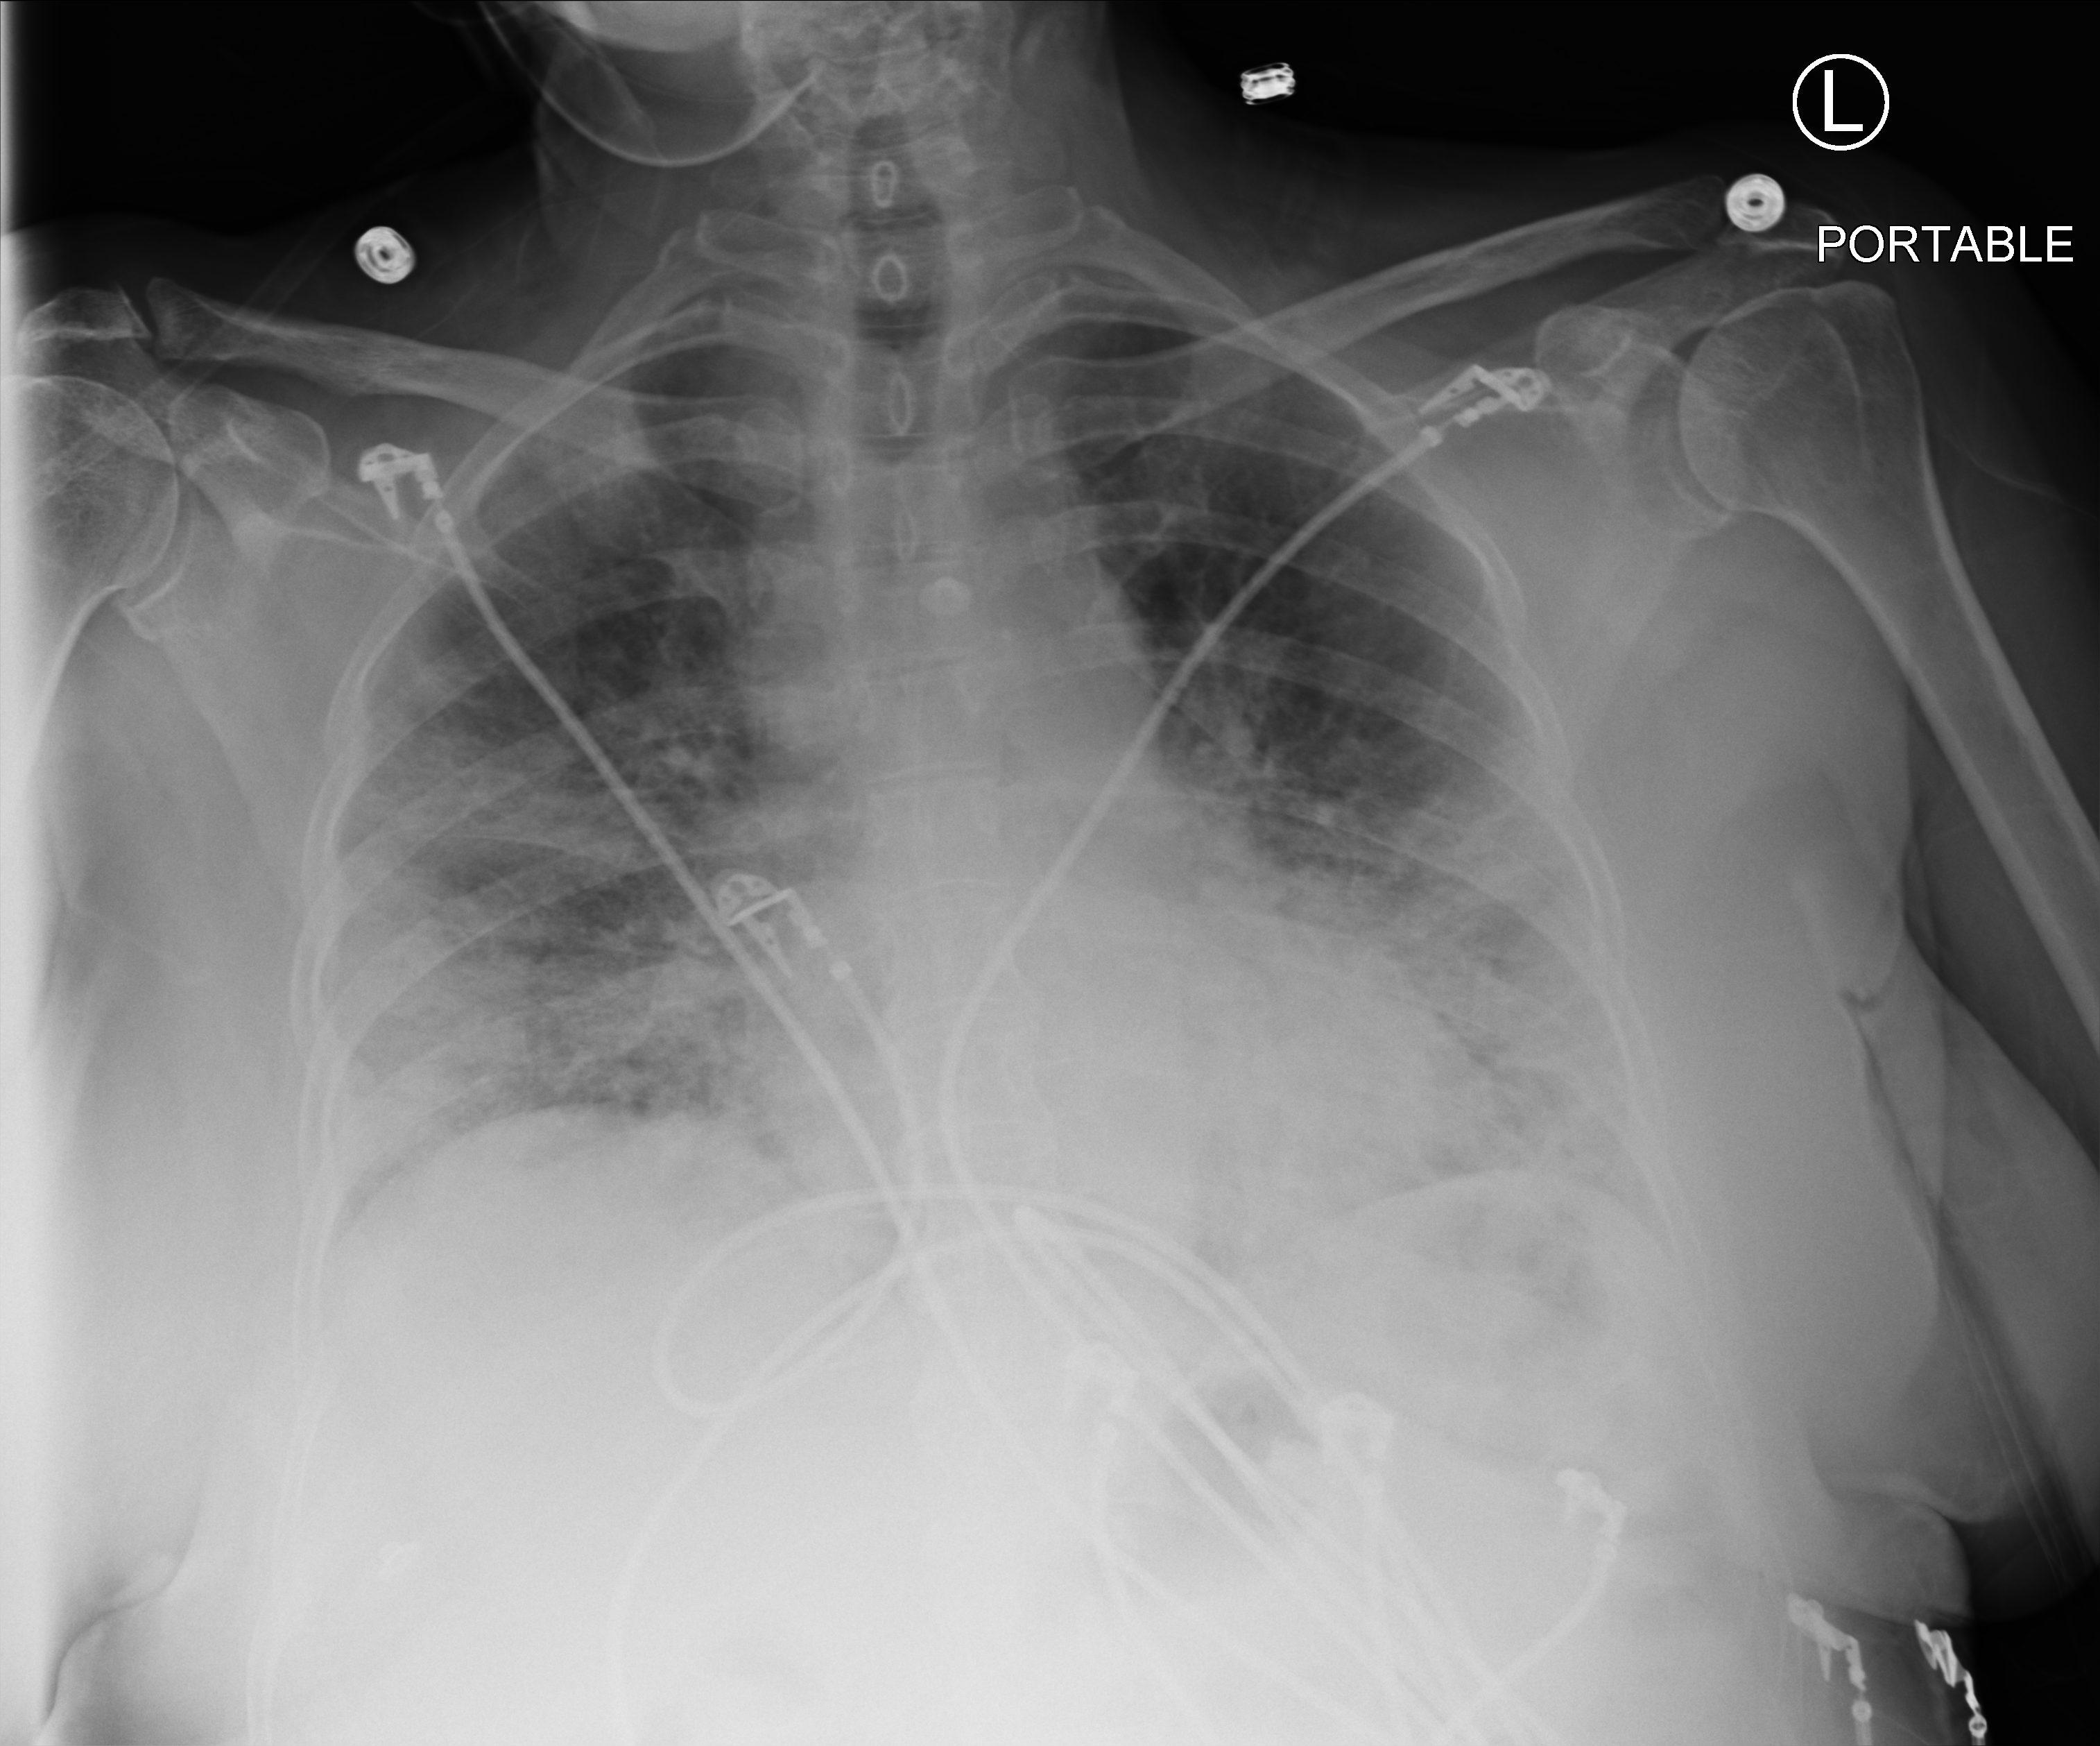
Chest X-ray (portable), anteroposterior (AP) projection. Patient hospitalised with COVID-19; female, aged 60–74 years.
Hospital-stay facts (about this admission, not read from this image; timing relative to this image not recorded): mechanically ventilated during this hospital stay: yes; hypertension (admission record): yes.